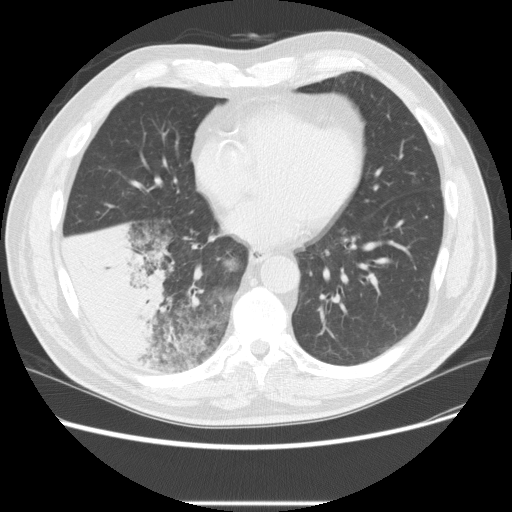
Low-dose screening chest CT, one axial slice. Slice 90 of 233 in the series (ordered by position). Lung window (W 1500 / L -600 HU). 512 × 512 image matrix, field of view 380 × 380 mm.
Annotated regions visible in this slice (expert manual segmentation):
- lesion 3 (tumor, lower lobe of right lung): bounding box <66,218,172,357> (left, top, right, bottom; pixels)